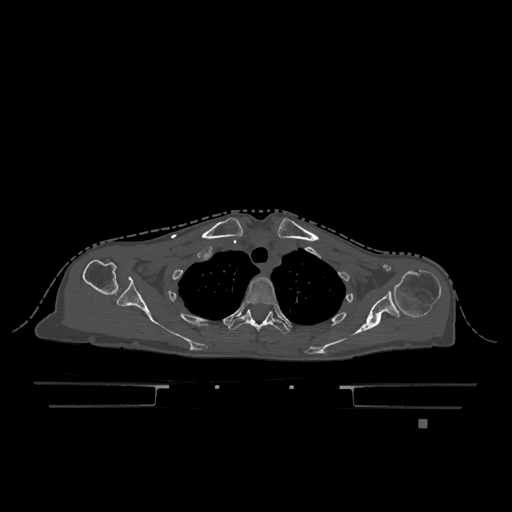
CT including the spine, one axial slice. Slice 941 of 1317 in the series (ordered by position). Bone window (W 1800 / L 400 HU). 512 × 512 image matrix, field of view 500 × 500 mm. Female patient, age 74 years. Case-level facts recorded for this patient, not image findings: primary cancer: lung.
Structures marked on this image (semi-automatic segmentation, software-assisted and operator-edited):
- T2 vertebra: bounding box (x1, y1, x2, y2) in pixels: (246, 277, 276, 305)
- T3 vertebra: (229, 309, 290, 335)